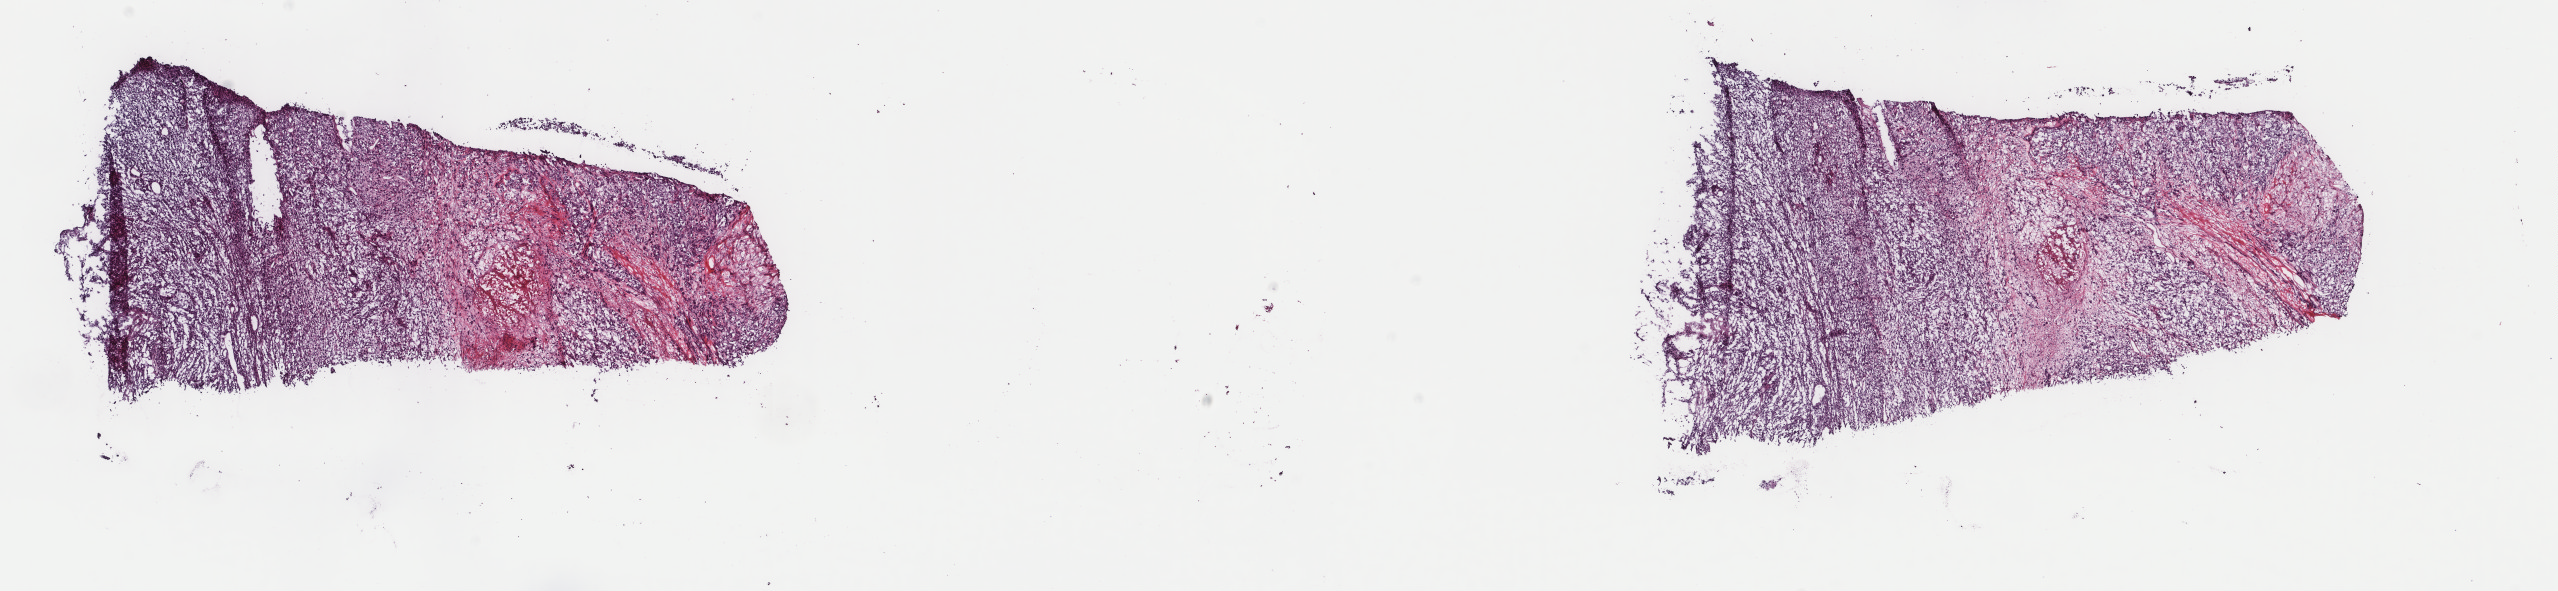
H&E whole-slide image — a low-resolution overview of the entire scanned area, about 20.3 x 4.7 mm (acquisition: 40x scan); frozen section from the top of the tissue portion; metastatic tumour sample. Patient: female, age at initial diagnosis 38 years. Slide review estimates, as recorded: tumour cells 90%, tumour nuclei 90%, normal cells 0%, stromal cells 6%, necrosis 4%. Infiltration values recorded for this section: lymphocyte infiltration 2%, monocyte infiltration 1%, neutrophil infiltration 0%.
This section: metastatic tumour tissue. Patient diagnosis: Malignant melanoma, NOS.